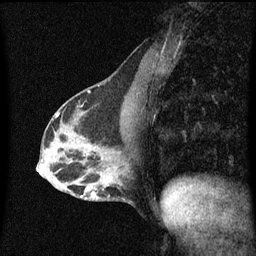
Breast MRI (dynamic contrast-enhanced), one sagittal slice; position 27 of 60 along the scan axis; dynamic contrast-enhanced series, image 2 of 3 at this slice position (ordered by acquisition); 1.5 T; TE 4.2 ms, TR 8.4 ms; 2 mm slice thickness; 256 × 256 image matrix, field of view 200 × 200 mm. Female patient, age 40 years.
Outlined on this slice (semi-automatic segmentation, software-assisted and operator-edited):
- analysis volume of interest (the breast-tissue region the enhancement analysis was run in; not a lesion): bounding box [x1, y1, x2, y2] px = [78, 166, 120, 201]
- tumour enhancement mask (voxels above the 70 % enhancement threshold inside the analysis volume of interest): [82, 178, 112, 199]